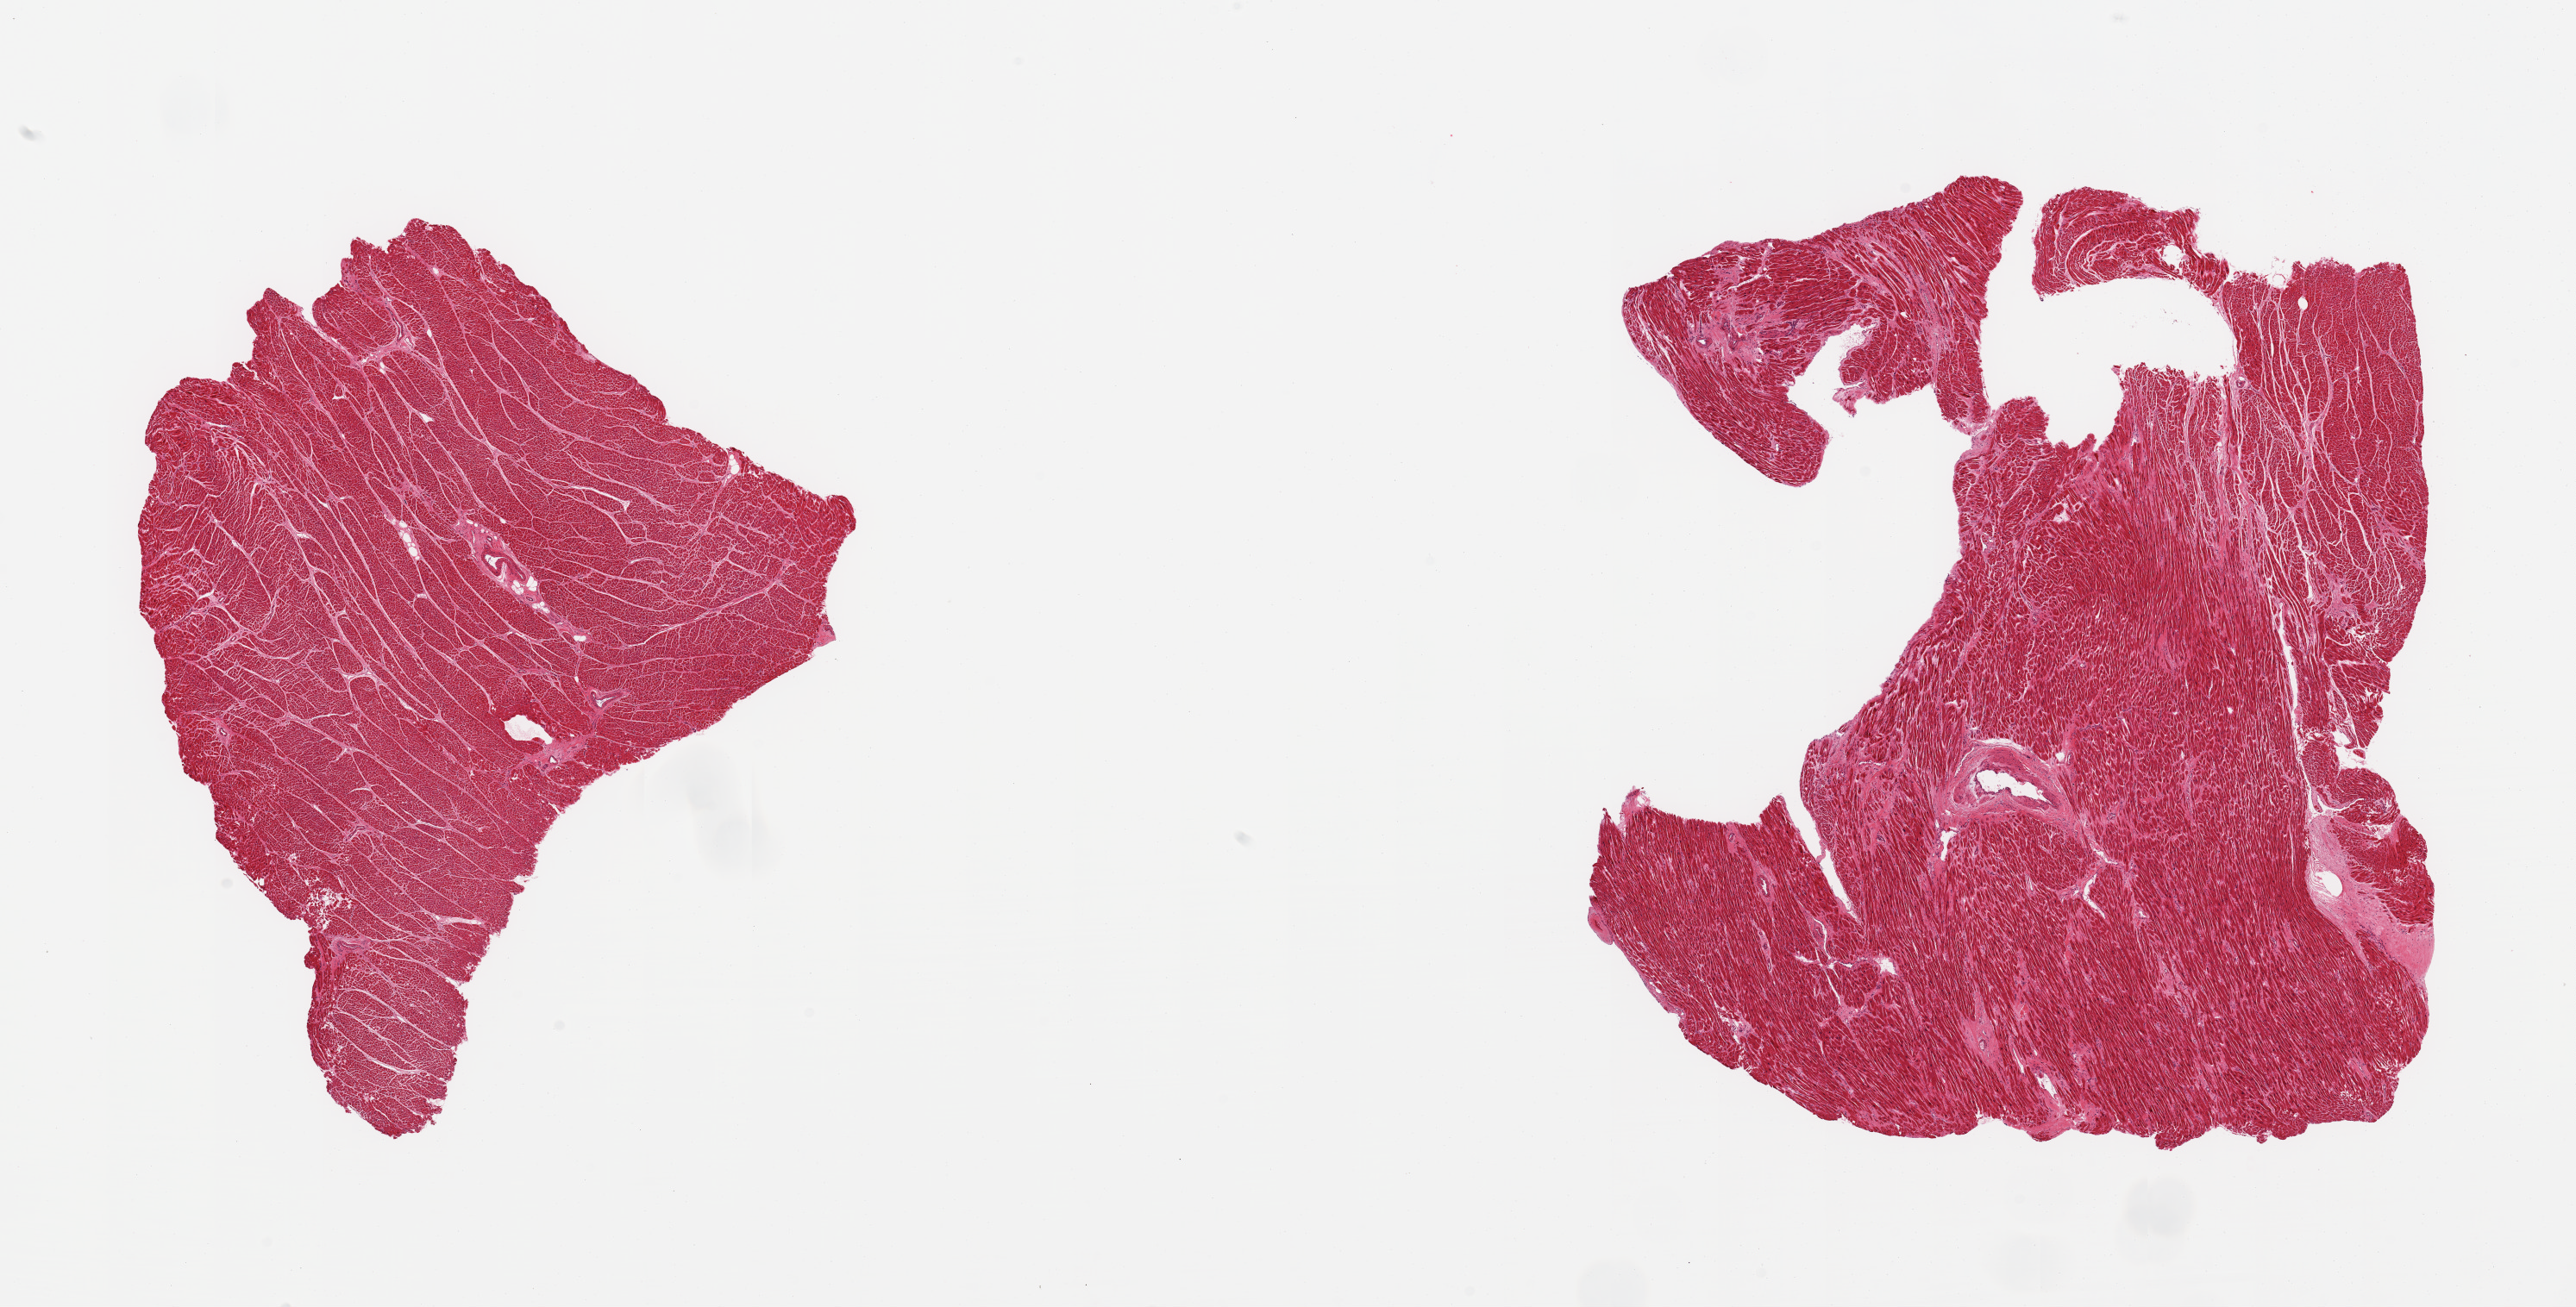
H&E whole-slide image, brightfield — a low-resolution overview of the entire scanned area, about 23.6 x 12.0 mm. PAXgene-fixed, paraffin-embedded tissue. Section of heart (target tissue). Tissue donor sample. Female donor.
Pathologist's review note for this sample: 2 pieces; mild patchy fibrosis.